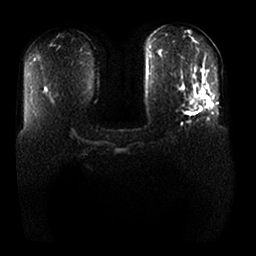
Breast MRI, one axial slice; diffusion-weighted series; image 2 of 4 stored at this slice position (different b-values; order by instance number); 1.5 T; 256 × 256 image matrix. Female patient.
Outlined on this slice (outlined manually by an expert reader):
- tumour on diffusion-weighted imaging: bounding box (x1, y1, x2, y2) in pixels: (188, 97, 210, 112)